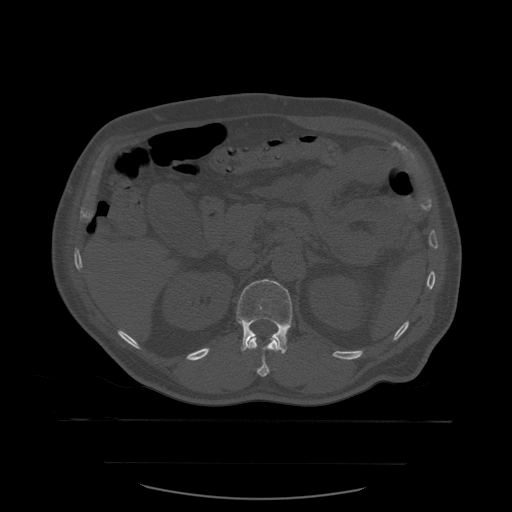
CT including the spine, one axial slice; slice 256 of 590 in the series (ordered by position); bone window (W 1800 / L 400 HU); 512 × 512 image matrix. Patient age 71 years. Case-level facts recorded for this patient, not image findings: primary cancer: lung; vertebrae with lytic lesions (as recorded): T1, T2, L5, S1.
Structures marked on this image (semi-automatic segmentation, software-assisted and operator-edited):
- L1 vertebra: box from (x=237, y=279) to (x=293, y=354) px
- T12 vertebra: (x=241, y=336)–(x=284, y=377)